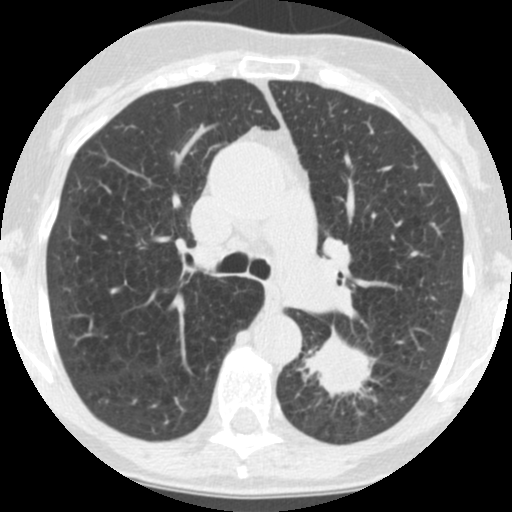
Low-dose screening chest CT, axial slice; third screening round (two years after baseline); lung window (W 1500 / L -600 HU); 2.5 mm slice thickness; standard (soft-tissue) reconstruction kernel (STANDARD); 120 kVp. Female participant, aged 71 years at enrolment.
Expert-annotated lung lesion, bounding box <302,328,383,410> (left, top, right, bottom; pixels). The screening reader recorded 2 non-calcified nodules or masses ≥4 mm on this exam; which of them this box marks is not recorded. Lung cancer was diagnosed 26 days after this screen: squamous cell carcinoma, NOS, left lower lobe, poorly differentiated (G3), stage IB (AJCC 6th edition), 40 mm at pathology.